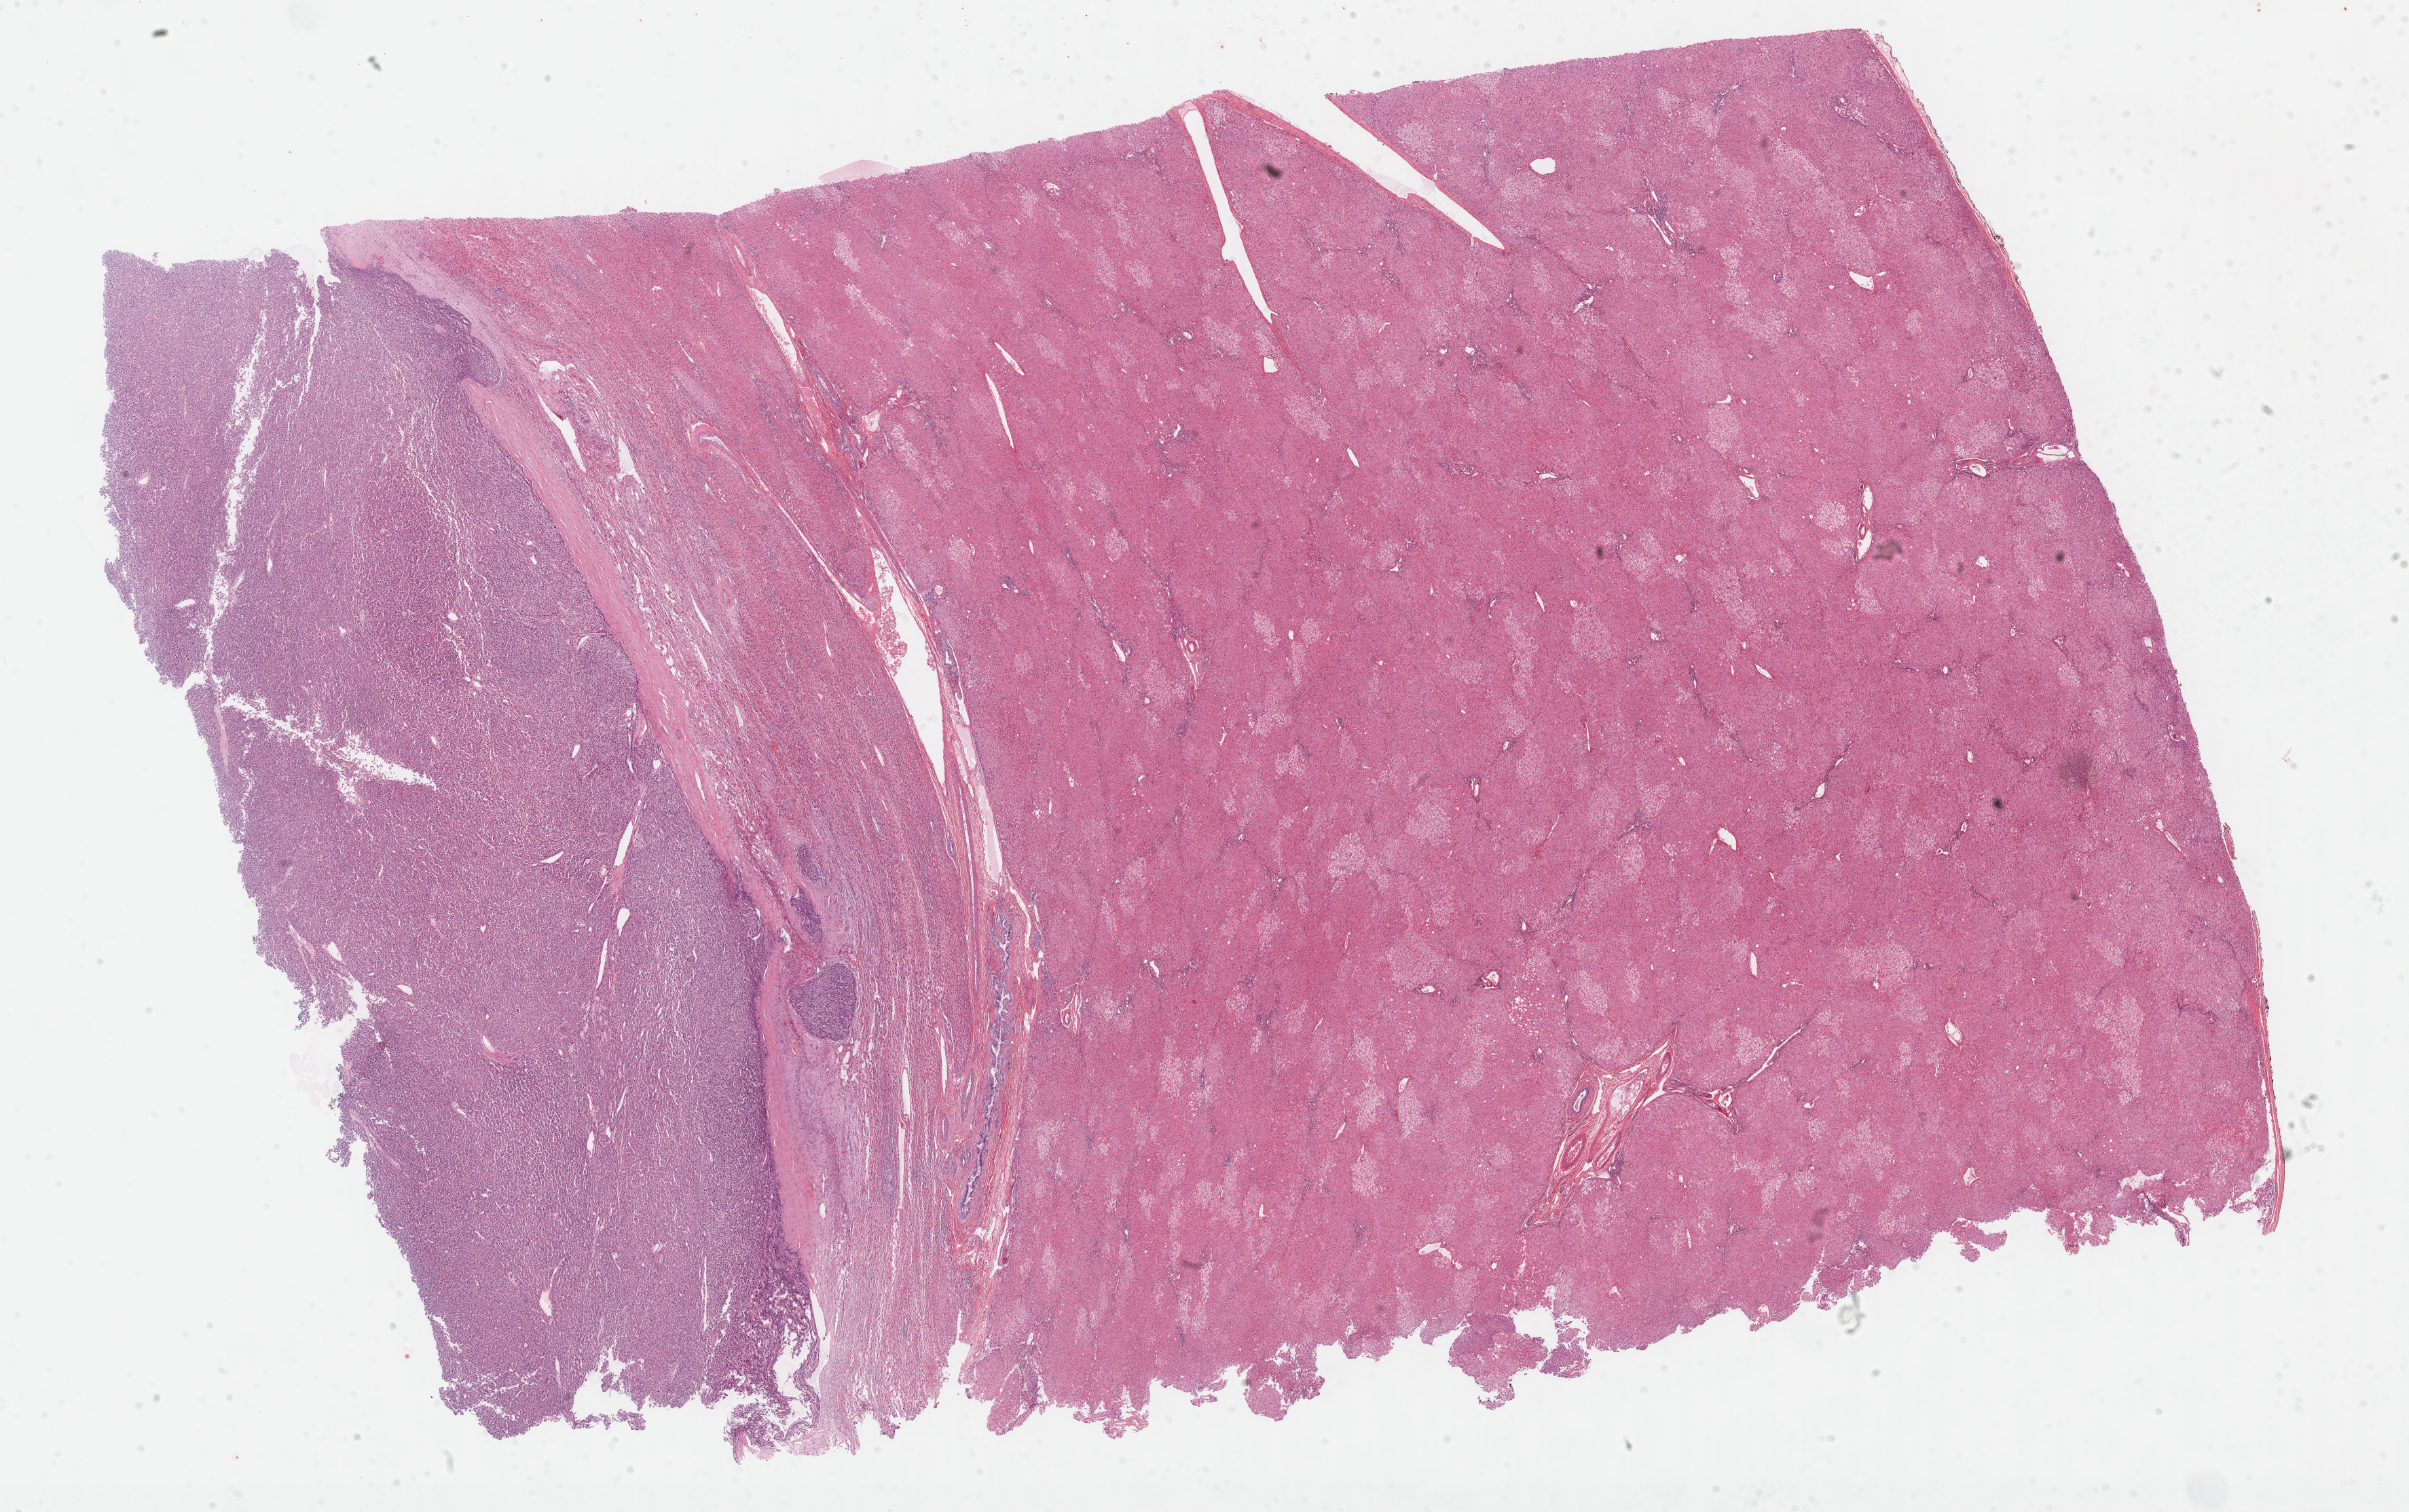
Digitized H&E tissue section (whole slide) — shown as a low-resolution overview of the whole scanned area (about 28.7 x 18.0 mm, from a 40x scan). FFPE section. Sample: primary tumour, liver. Patient: male, age at initial diagnosis 24 years. Histologic grade: G3 (poorly differentiated).
Histologic diagnosis: Hepatocellular carcinoma, NOS. AJCC pathologic stage: II (7th edition). TNM: T2 NX MX.